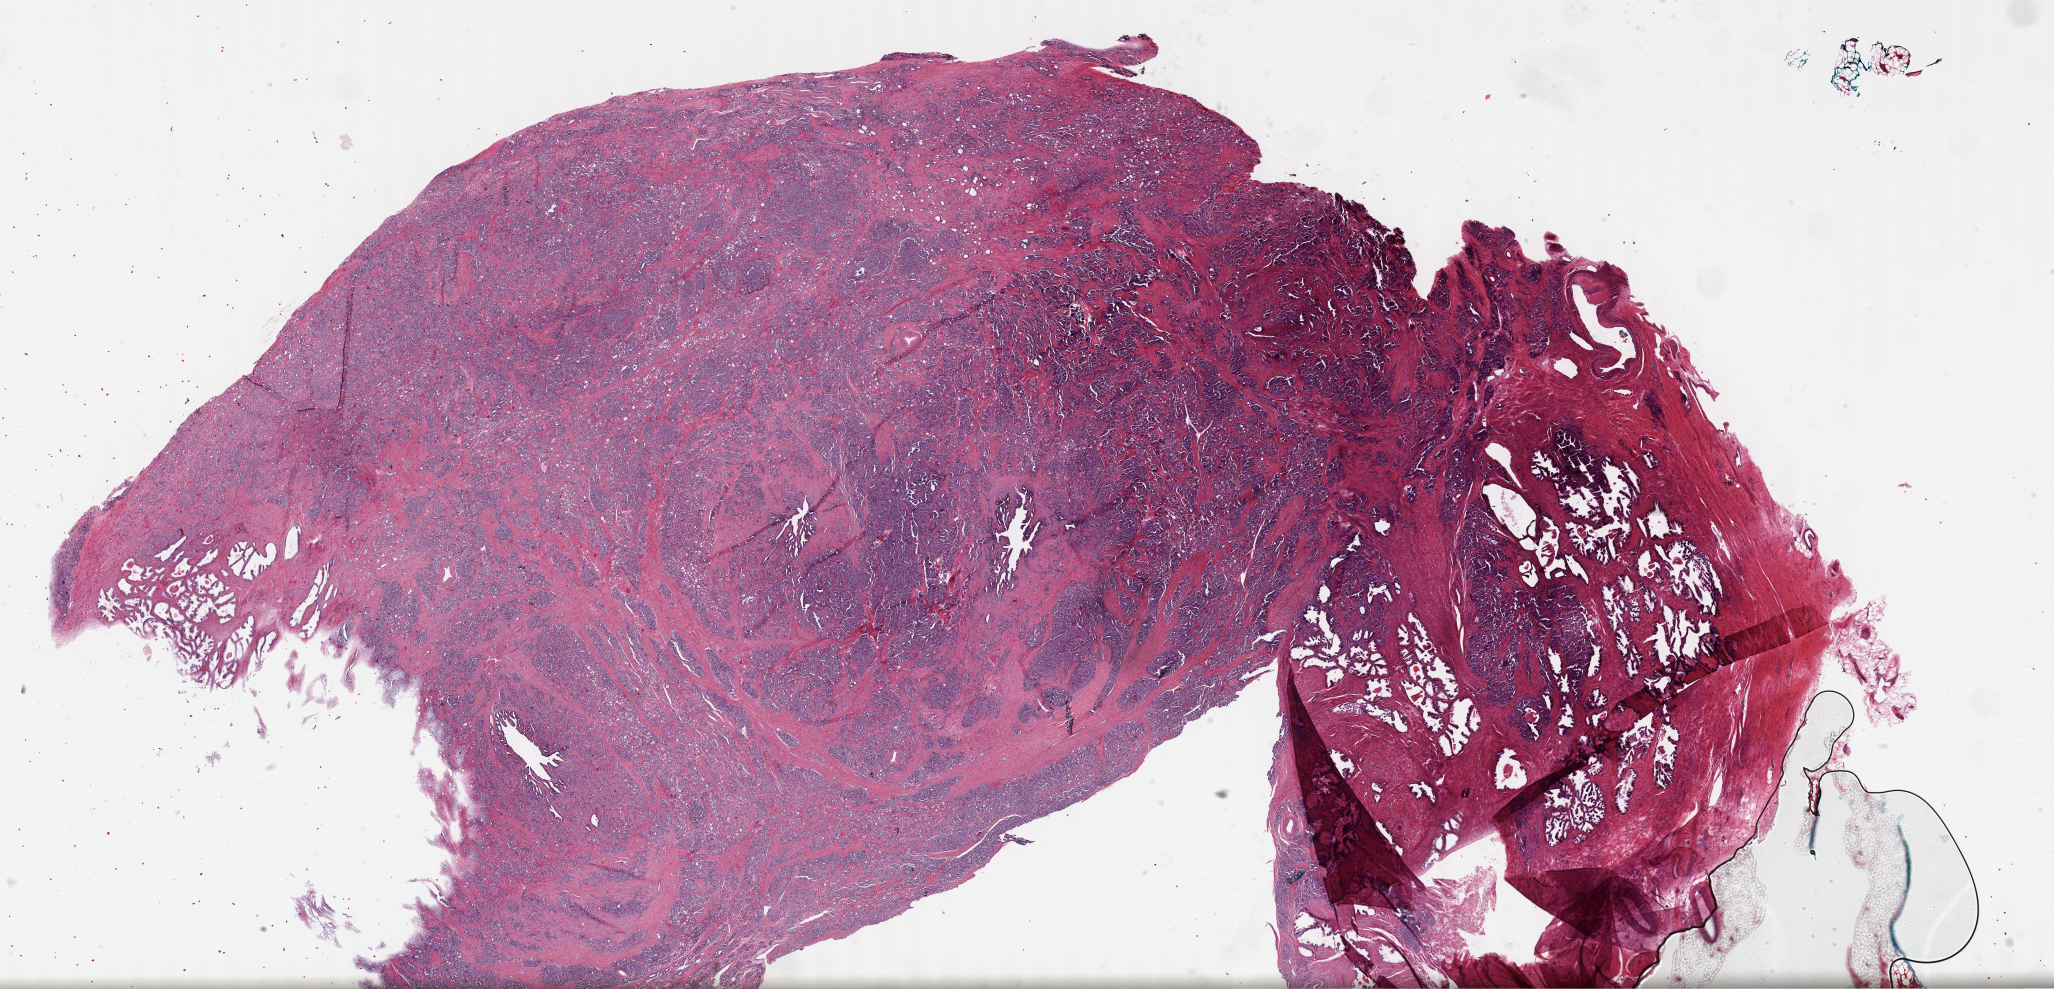
H&E whole-slide image, a low-resolution overview of the entire scanned area, about 33.2 x 16.0 mm, FFPE section, primary tumour sample from the prostate. Patient: male, age at initial diagnosis 47 years. Gleason score: 9 (4+5).
Pathologic diagnosis: Adenocarcinoma, NOS (prostate gland). Laterality: bilateral.